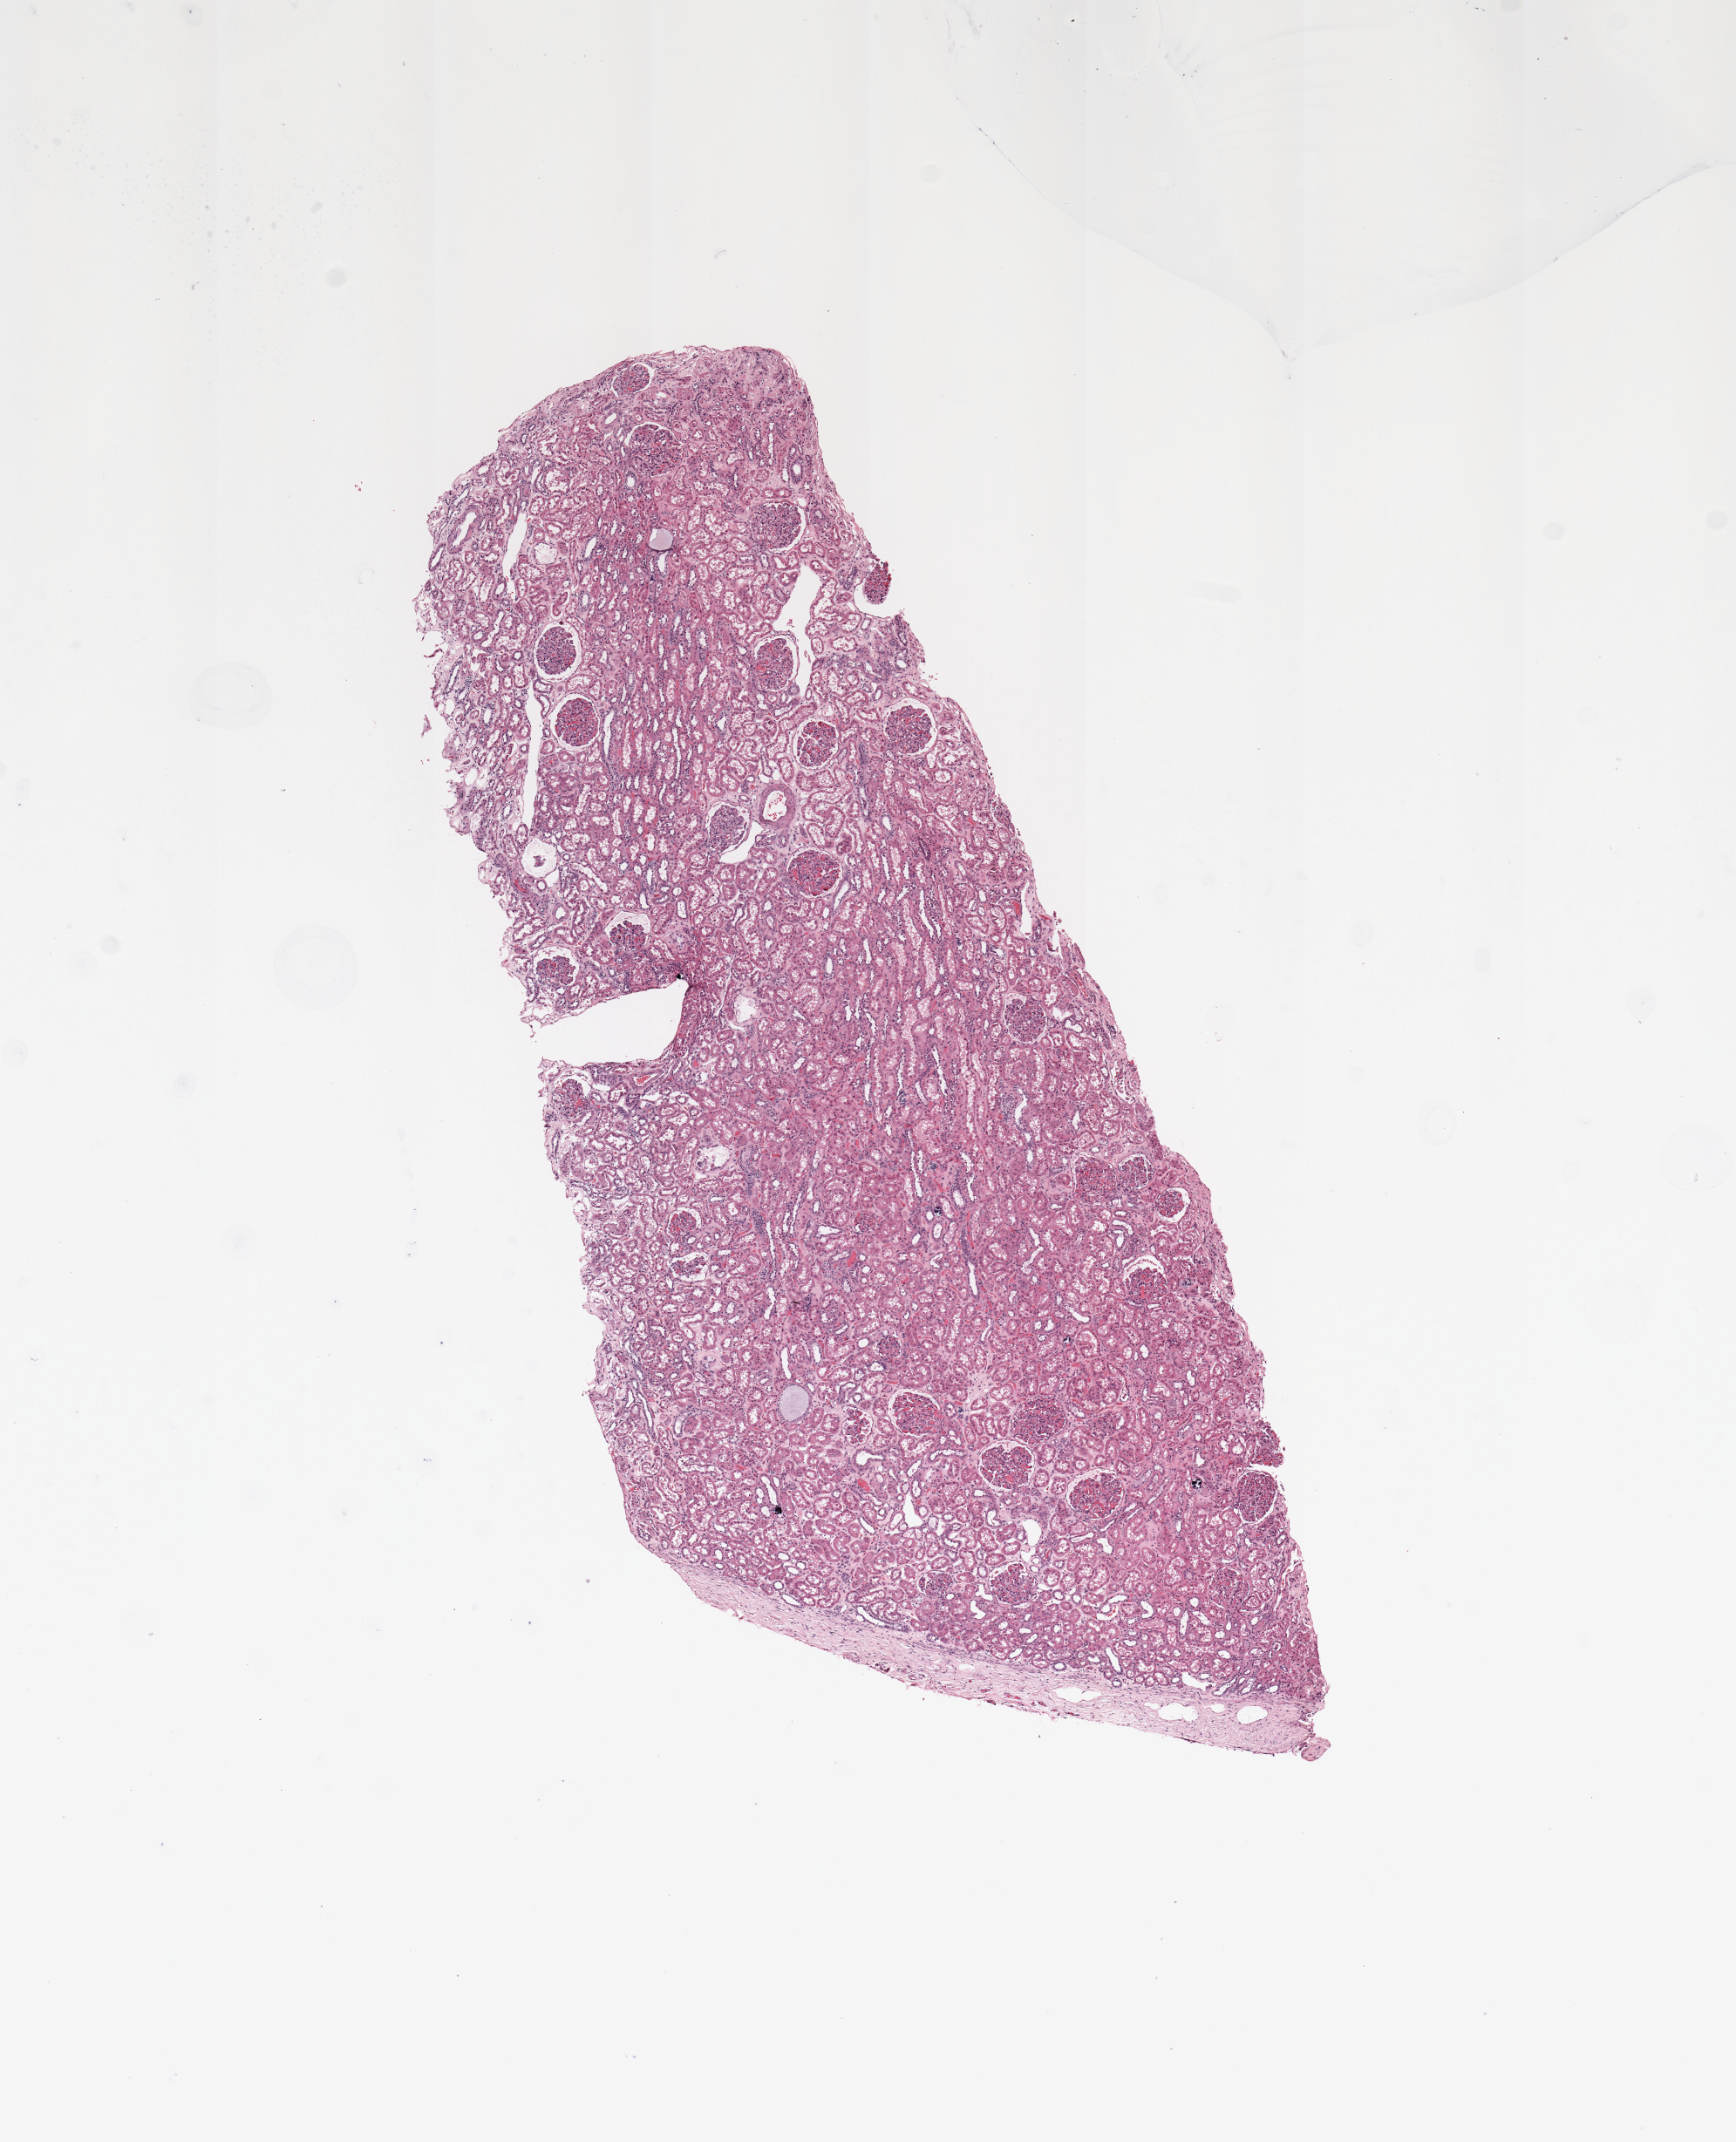
Digitized Hematoxylin and eosin (H&E) stained tissue section (whole slide) — low-resolution overview of the scanned area, about 7.9 x 9.7 mm (slide scanned at 20x), normal (non-tumour) tissue sample, sampled site: kidney. 53-year-old male patient.
This section: normal (non-tumour) tissue from the same patient. Patient diagnosis: Renal cell carcinoma, NOS.